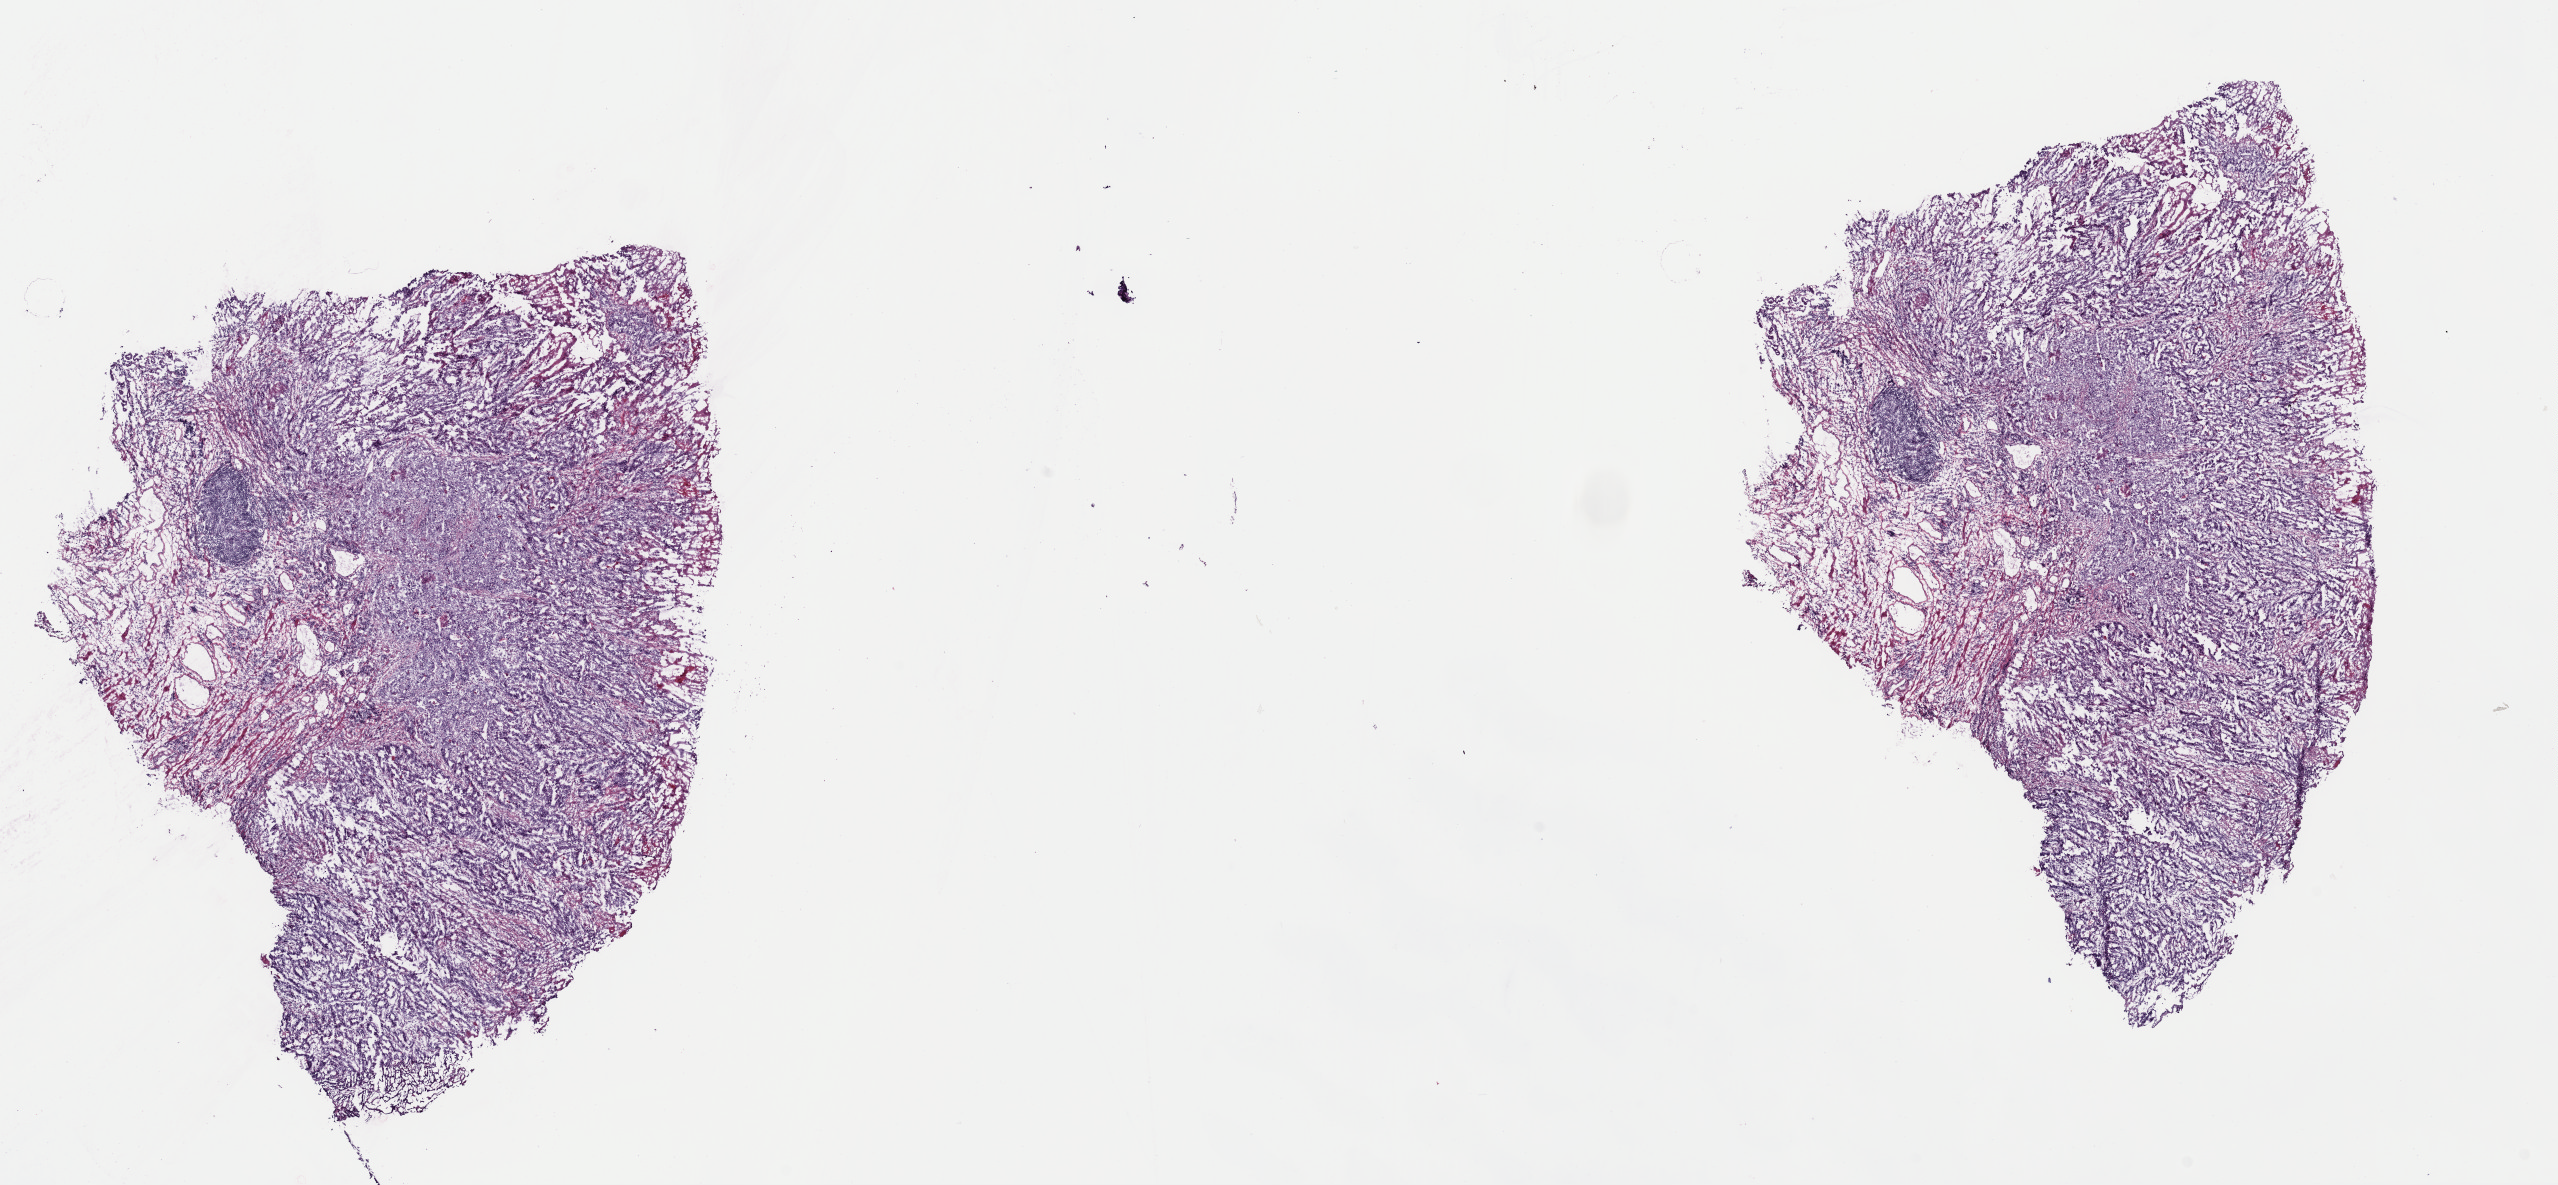
H&E-stained whole-slide image — low-resolution overview of the scanned area, about 20.2 x 9.4 mm. Frozen section from the top of the tissue portion. Sample: primary tumour, esophagus. Patient: male, age at initial diagnosis 75 years. Histologic grade: GX (grade cannot be assessed). Composition of this section per pathologist review: tumour cells 100%, tumour nuclei 80%, normal cells 0%, stromal cells 0%, necrosis 0%. Infiltration values recorded for this section: lymphocyte infiltration 6%, monocyte infiltration 0%, neutrophil infiltration 1%.
- diagnosis: Adenocarcinoma, NOS
- lymph nodes positive (case pathology): 6 of 12 examined
- AJCC pathologic stage: IIIA (7th edition)
- TNM: T2 N2 MX